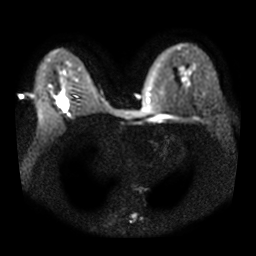
Breast MRI, one axial slice; slice 18 of 31 in the series (ordered by position); diffusion-weighted series; image 2 of 4 stored at this slice position (different b-values; order by instance number); 3 T; 5 mm slice thickness; 256 × 256 image matrix, field of view 340 × 340 mm. Female patient.
Outlined on this slice (outlined manually by an expert reader):
- tumour on diffusion-weighted imaging: bounding box [x1, y1, x2, y2] px = [63, 97, 68, 110]